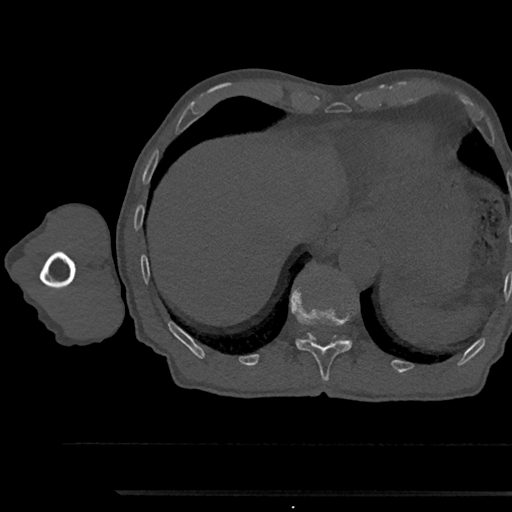
CT including the spine, one axial slice. Slice 769 of 797 in the series (ordered by position). 120 kVp. Bone window (W 1800 / L 400 HU). 512 × 512 image matrix, field of view 367 × 367 mm. Male patient, age 79 years. From the clinical record (not read from this slice): primary cancer: prostate.
Annotated regions visible in this slice (semi-automatic segmentation, software-assisted and operator-edited):
- T11 vertebra: bounding box [x1, y1, x2, y2] px = [292, 293, 352, 382]
- T12 vertebra: [308, 334, 346, 338]